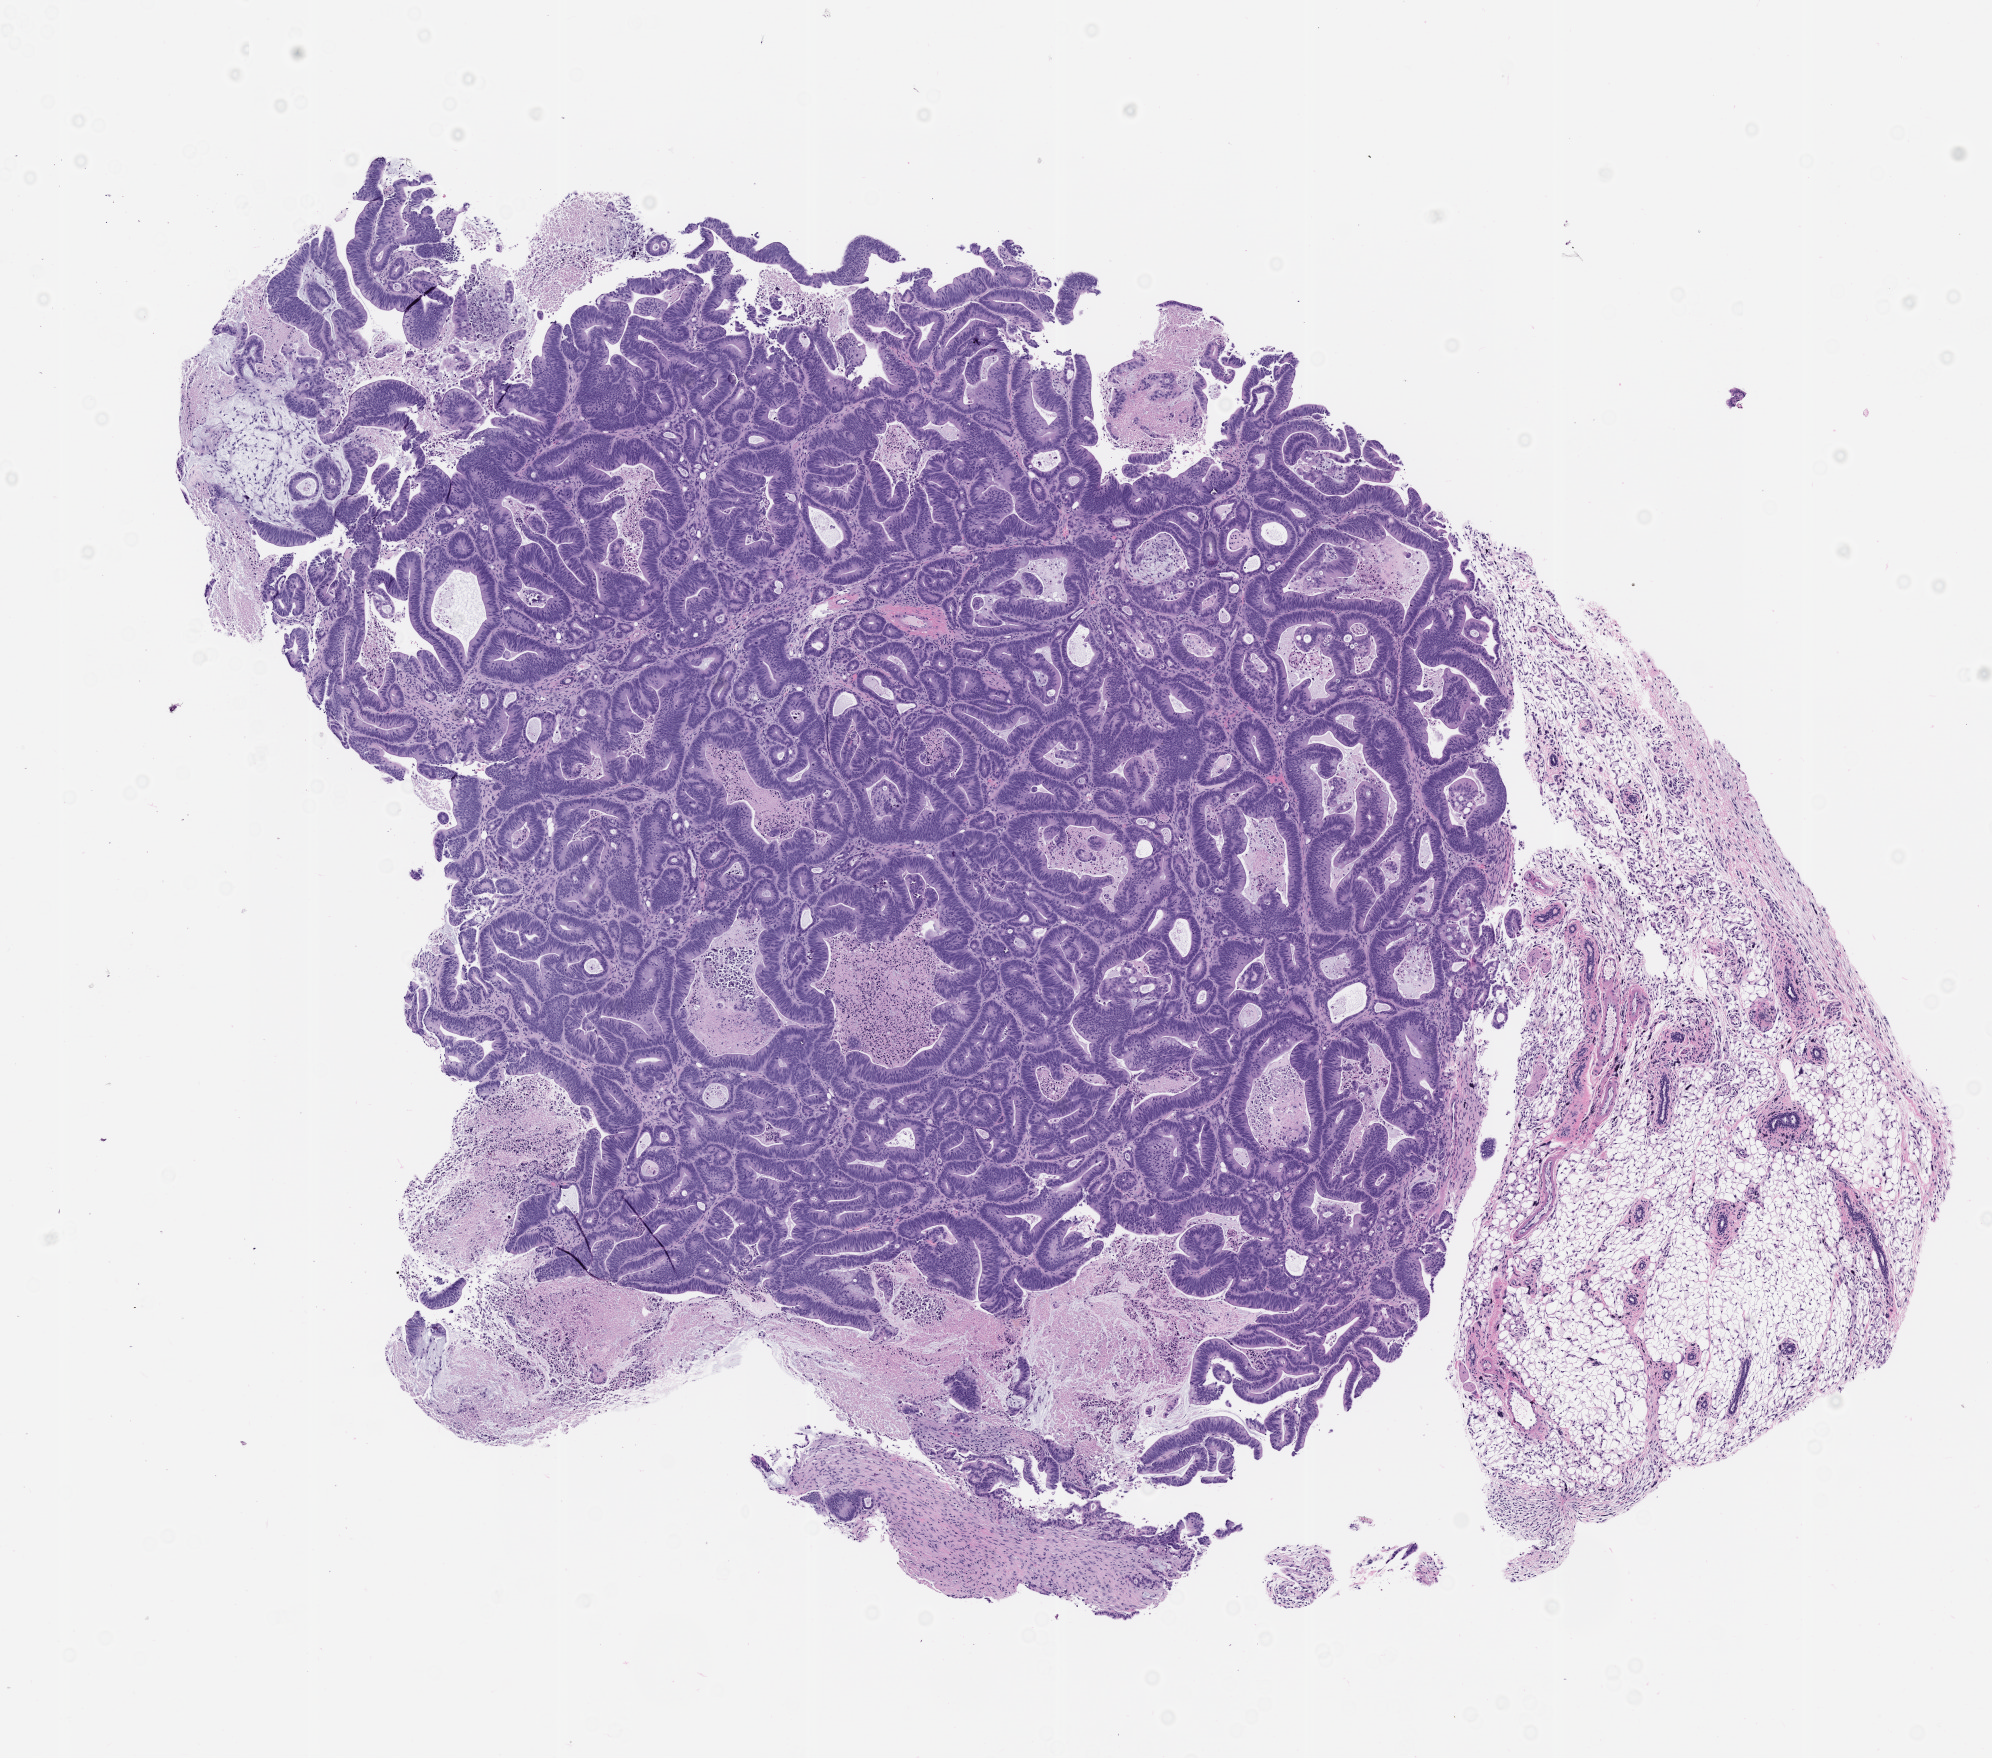
Hematoxylin and eosin (H&E) whole-slide image of a patient-derived xenograft (PDX) tumor grown in a mouse, passage 2, shown as a low-resolution overview of the whole scanned area (about 8.0 x 7.1 mm); FFPE section; originating tumor site category: colon.
Originating patient diagnosis: Colon Adenocarcinoma.